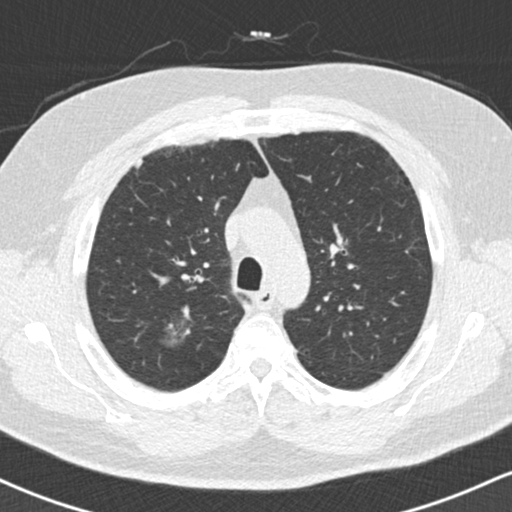
Low-dose screening chest CT, one axial slice. Slice 123 of 169 in the series (ordered by position). Reconstruction kernel B30f. 120 kVp. Lung window (W 1500 / L -600 HU). 2 mm slice thickness. 512 × 512 image matrix, field of view 320 × 320 mm.
Outlined on this slice (expert manual segmentation):
- lesion 1 (tumor, upper lobe of right lung): bounding box (x1, y1, x2, y2) in pixels: (162, 321, 193, 347)